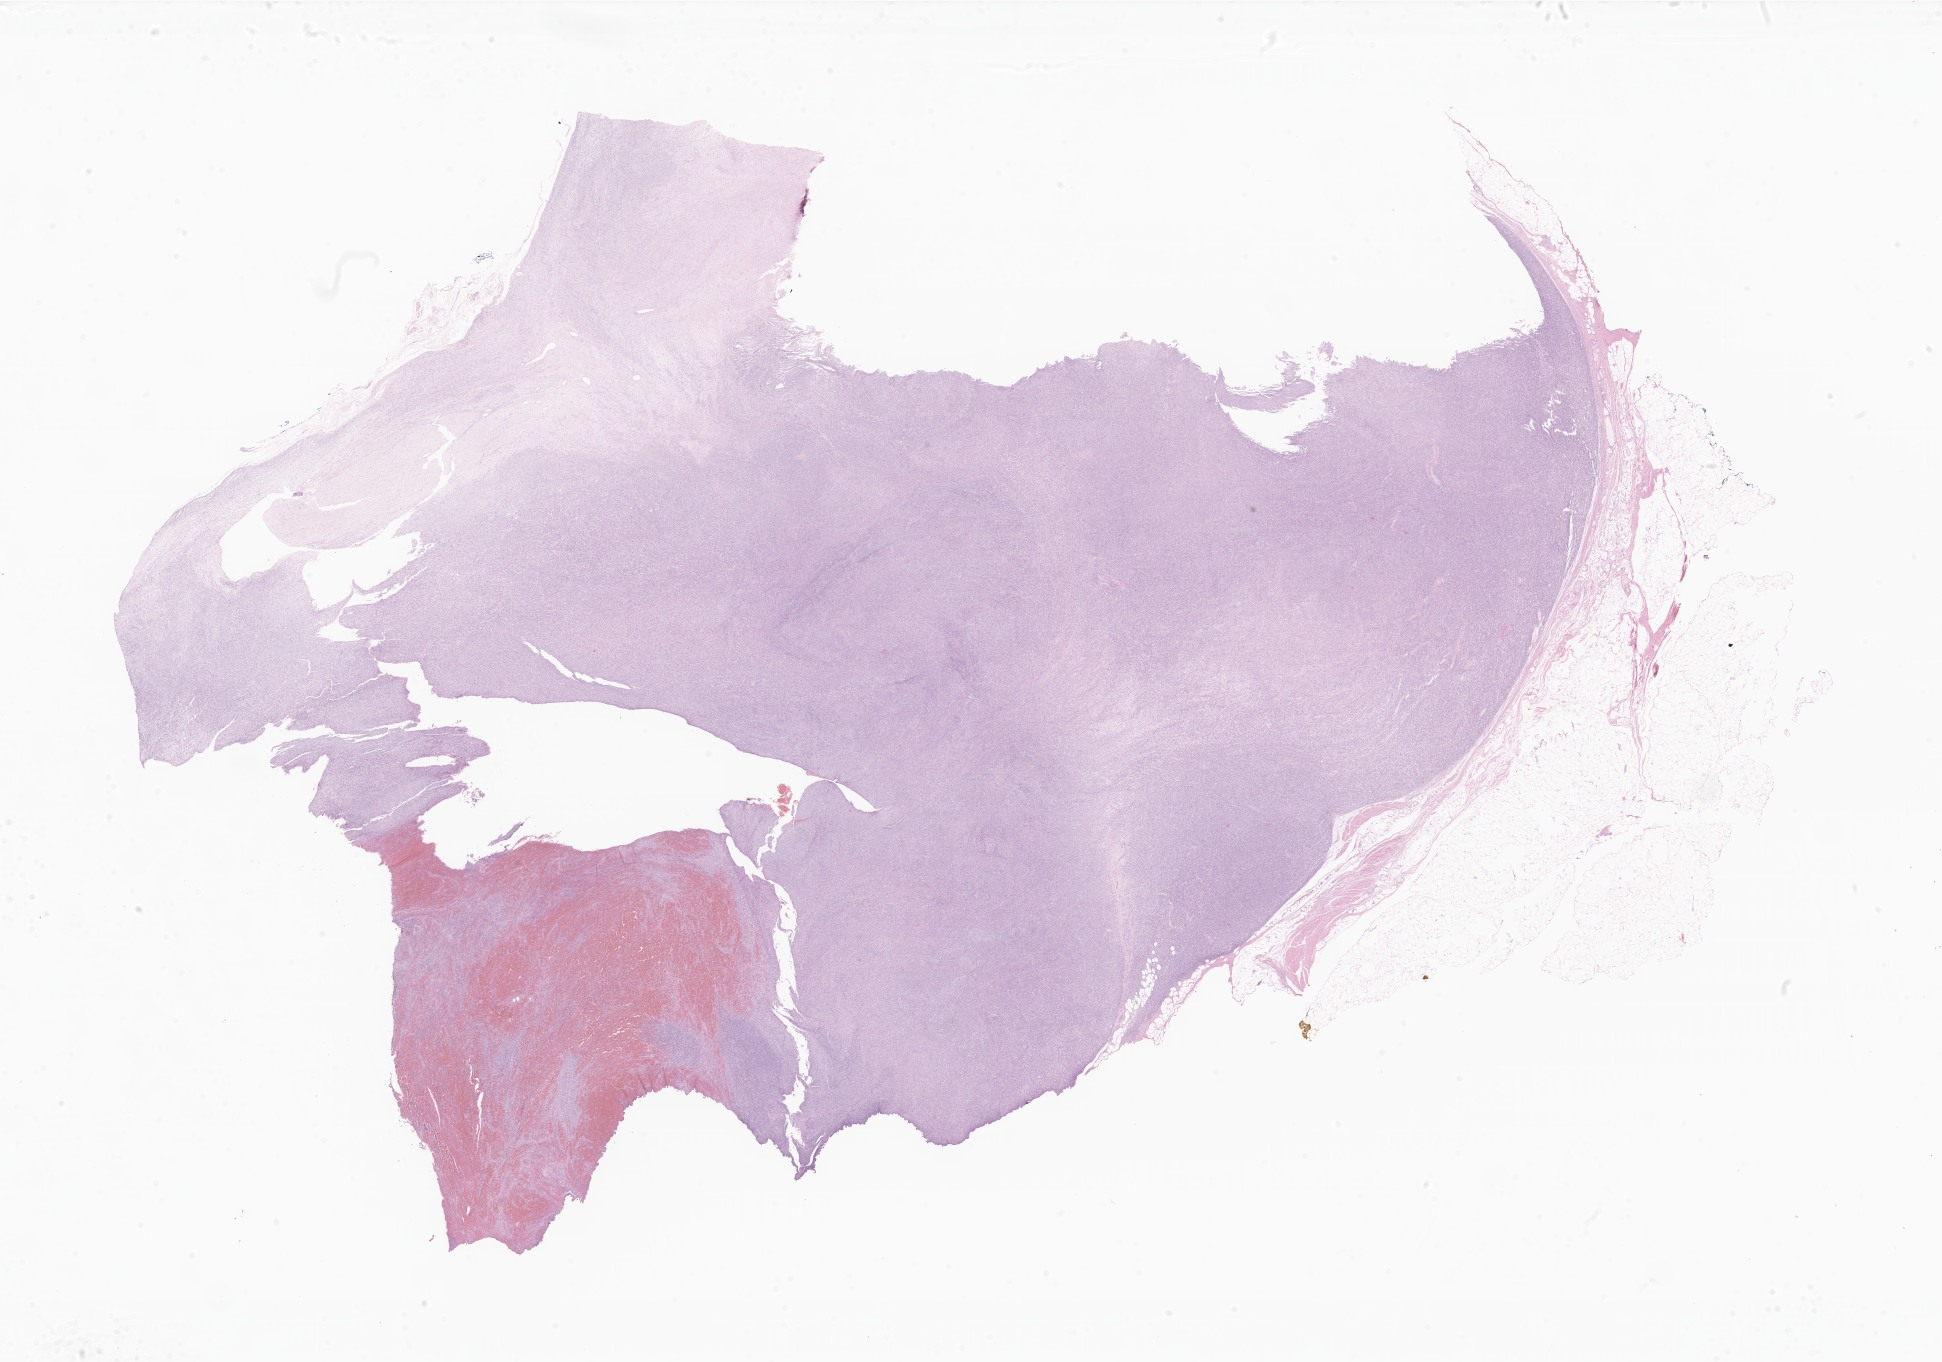
Digitized H&E-stained section of tumor tissue from the soft tissue of lower extremity — low-resolution overview of the scanned area, about 32.8 x 23.0 mm. Formalin-fixed, paraffin-embedded (FFPE) tissue. Patient female; age 83 months (6 years 11 months).
• tissue or organ of origin (case record): connective, subcutaneous and other soft tissues of lower limb and hip
• diagnosis (ICD-O-3 morphology term): Synovial sarcoma, spindle cell